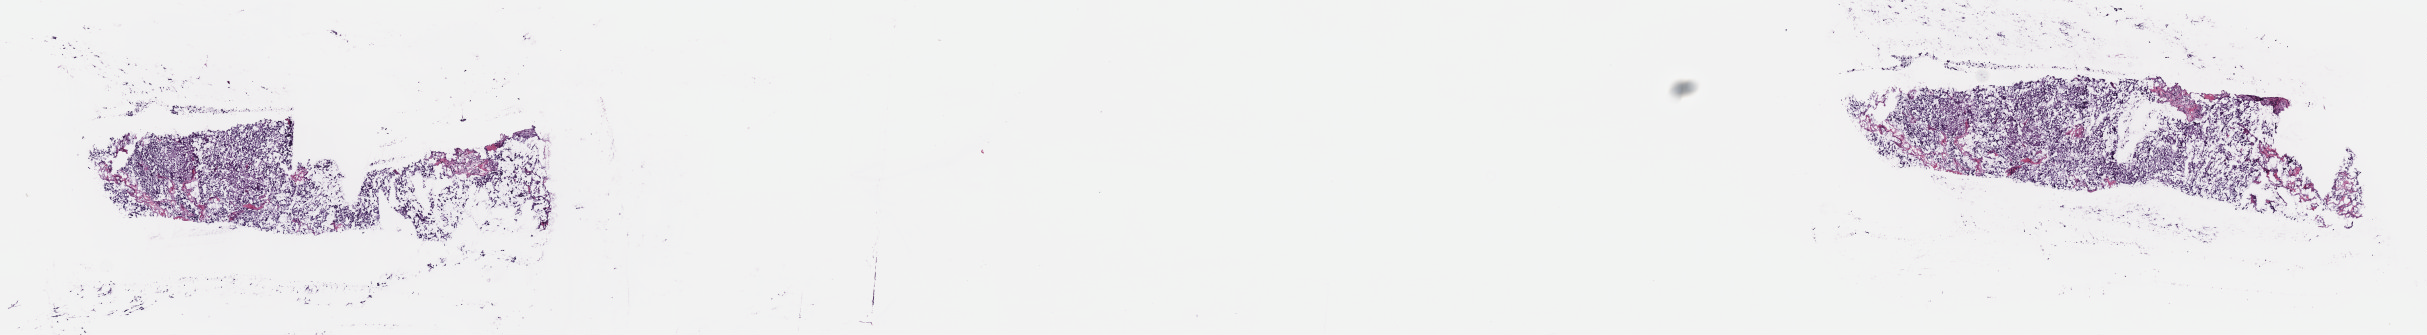
Digitized H&E tissue section (whole slide), shown as a low-resolution overview of the whole scanned area (about 19.6 x 2.7 mm, acquisition: 40x scan). Frozen section. Primary tumour sample from the adrenal gland. Male patient; age at initial diagnosis 44 years. Slide review estimates, as recorded: tumour cells 100%, tumour nuclei 75%, normal cells 0%, stromal cells 0%, necrosis 0%. Inflammatory infiltration, as recorded: lymphocyte infiltration 1%, monocyte infiltration 0%, neutrophil infiltration 0%.
Laterality: right. Diagnosis: Pheochromocytoma, malignant.